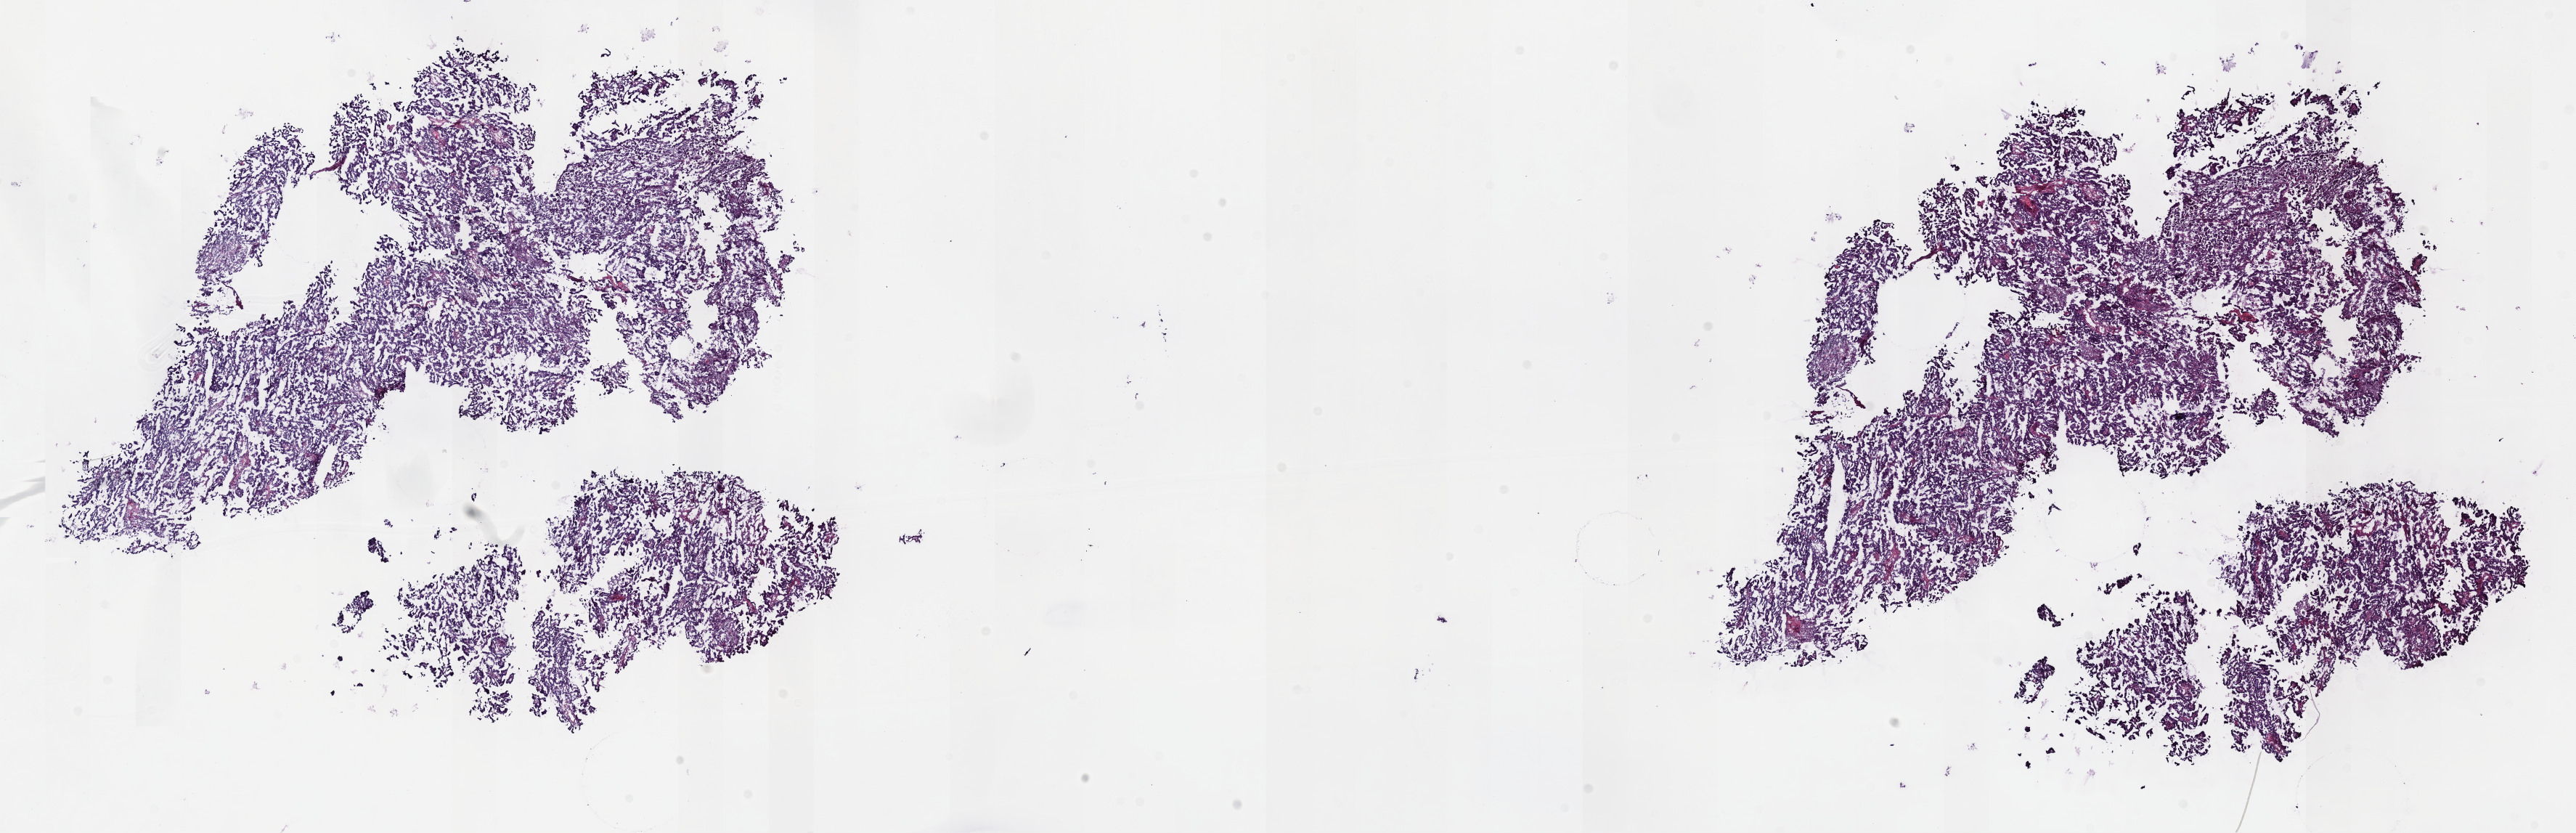
Hematoxylin and eosin (H&E) stained whole-slide image, whole scanned area (about 28.7 x 9.3 mm, from a 40x scan) shown as a low-resolution overview; frozen section; uterus, primary tumour sample. Female, age 73 years at initial diagnosis. Histologic grade: G3 (poorly differentiated). Composition of this section per pathologist review: tumour cells 80%, tumour nuclei 90%, normal cells 0%, stromal cells 20%, necrosis 0%. Inflammatory infiltration, as recorded: lymphocyte infiltration 0%, monocyte infiltration 0%, neutrophil infiltration 0%.
Histologic diagnosis: Serous surface papillary carcinoma (endometrium). FIGO stage: IA.